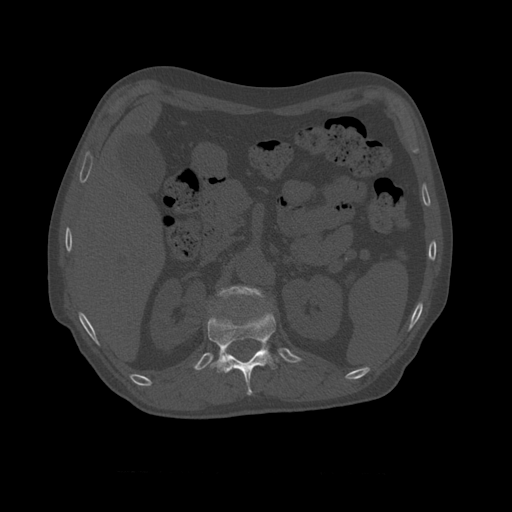
CT including the spine, one axial slice. Position 375 of 450 along the scan axis. 120 kVp. Bone window (W 1800 / L 400 HU). 1.25 mm slice thickness. 512 × 512 image matrix. Patient age 75 years. Case-level facts recorded for this patient, not image findings: primary cancer: prostate.
Annotated regions visible in this slice (semi-automatically segmented with operator editing):
- L1 vertebra: bounding box <218,286,265,299> (left, top, right, bottom; pixels)
- T11 vertebra: <207,312,279,396>